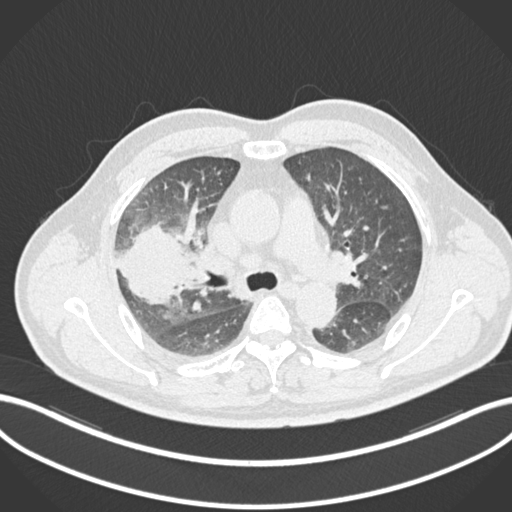
Chest CT, one axial slice; slice 651 of 852 in the series (ordered by position); reconstruction kernel B30f; 120 kVp; lung window (W 1500 / L -600 HU); 1 mm slice thickness; 512 × 512 image matrix, field of view 400 × 400 mm. Patient: male, 55 years. From the clinical record (not read from this slice): clinical TNM (as recorded): T3 N2 M1.
Annotated regions visible in this slice (bounding box drawn by a radiologist):
- lung tumour (recorded histology: adenocarcinoma): box from (x=119, y=223) to (x=194, y=307) px